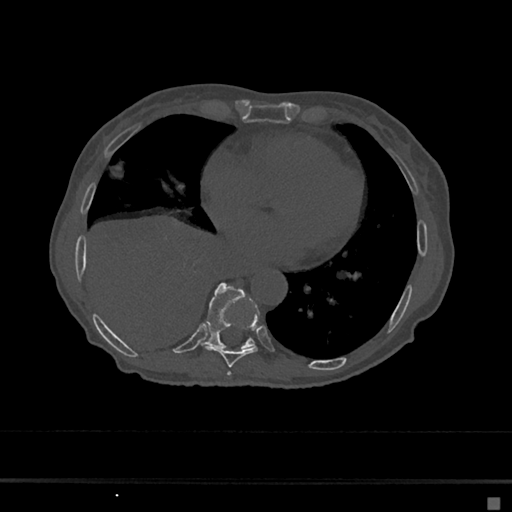
CT including the spine, one axial slice; slice 302 of 797 in the series (ordered by position); 120 kVp; bone window (W 1800 / L 400 HU); 512 × 512 image matrix, field of view 360 × 360 mm. Female patient, age 68 years. From the clinical record (not read from this slice): primary cancer: renal.
Structures marked on this image (semi-automatic segmentation, software-assisted and operator-edited):
- T7 vertebra: bounding box <228,372,231,376> (left, top, right, bottom; pixels)
- T8 vertebra: <205,308,259,367>
- T9 vertebra: <204,283,255,349>